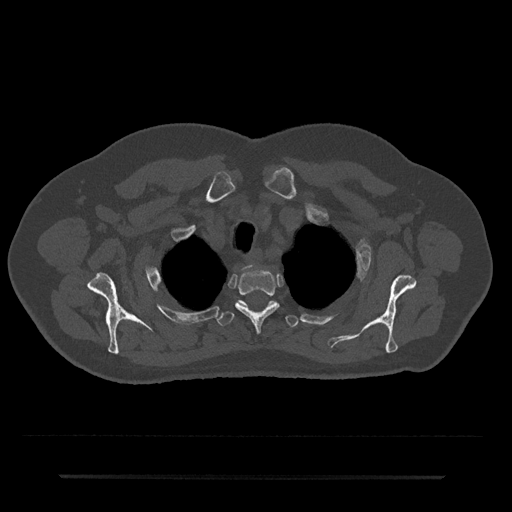
CT including the spine, one axial slice; slice 596 of 797 in the series (ordered by position); 120 kVp; bone window (W 1800 / L 400 HU); 512 × 512 image matrix, field of view 437 × 437 mm. Patient: male, 69 years. From the clinical record (not read from this slice): primary cancer: prostate.
Annotated regions visible in this slice (semi-automatic segmentation, software-assisted and operator-edited):
- T2 vertebra: bounding box (x1, y1, x2, y2) in pixels: (235, 269, 279, 332)
- T3 vertebra: (217, 300, 298, 328)